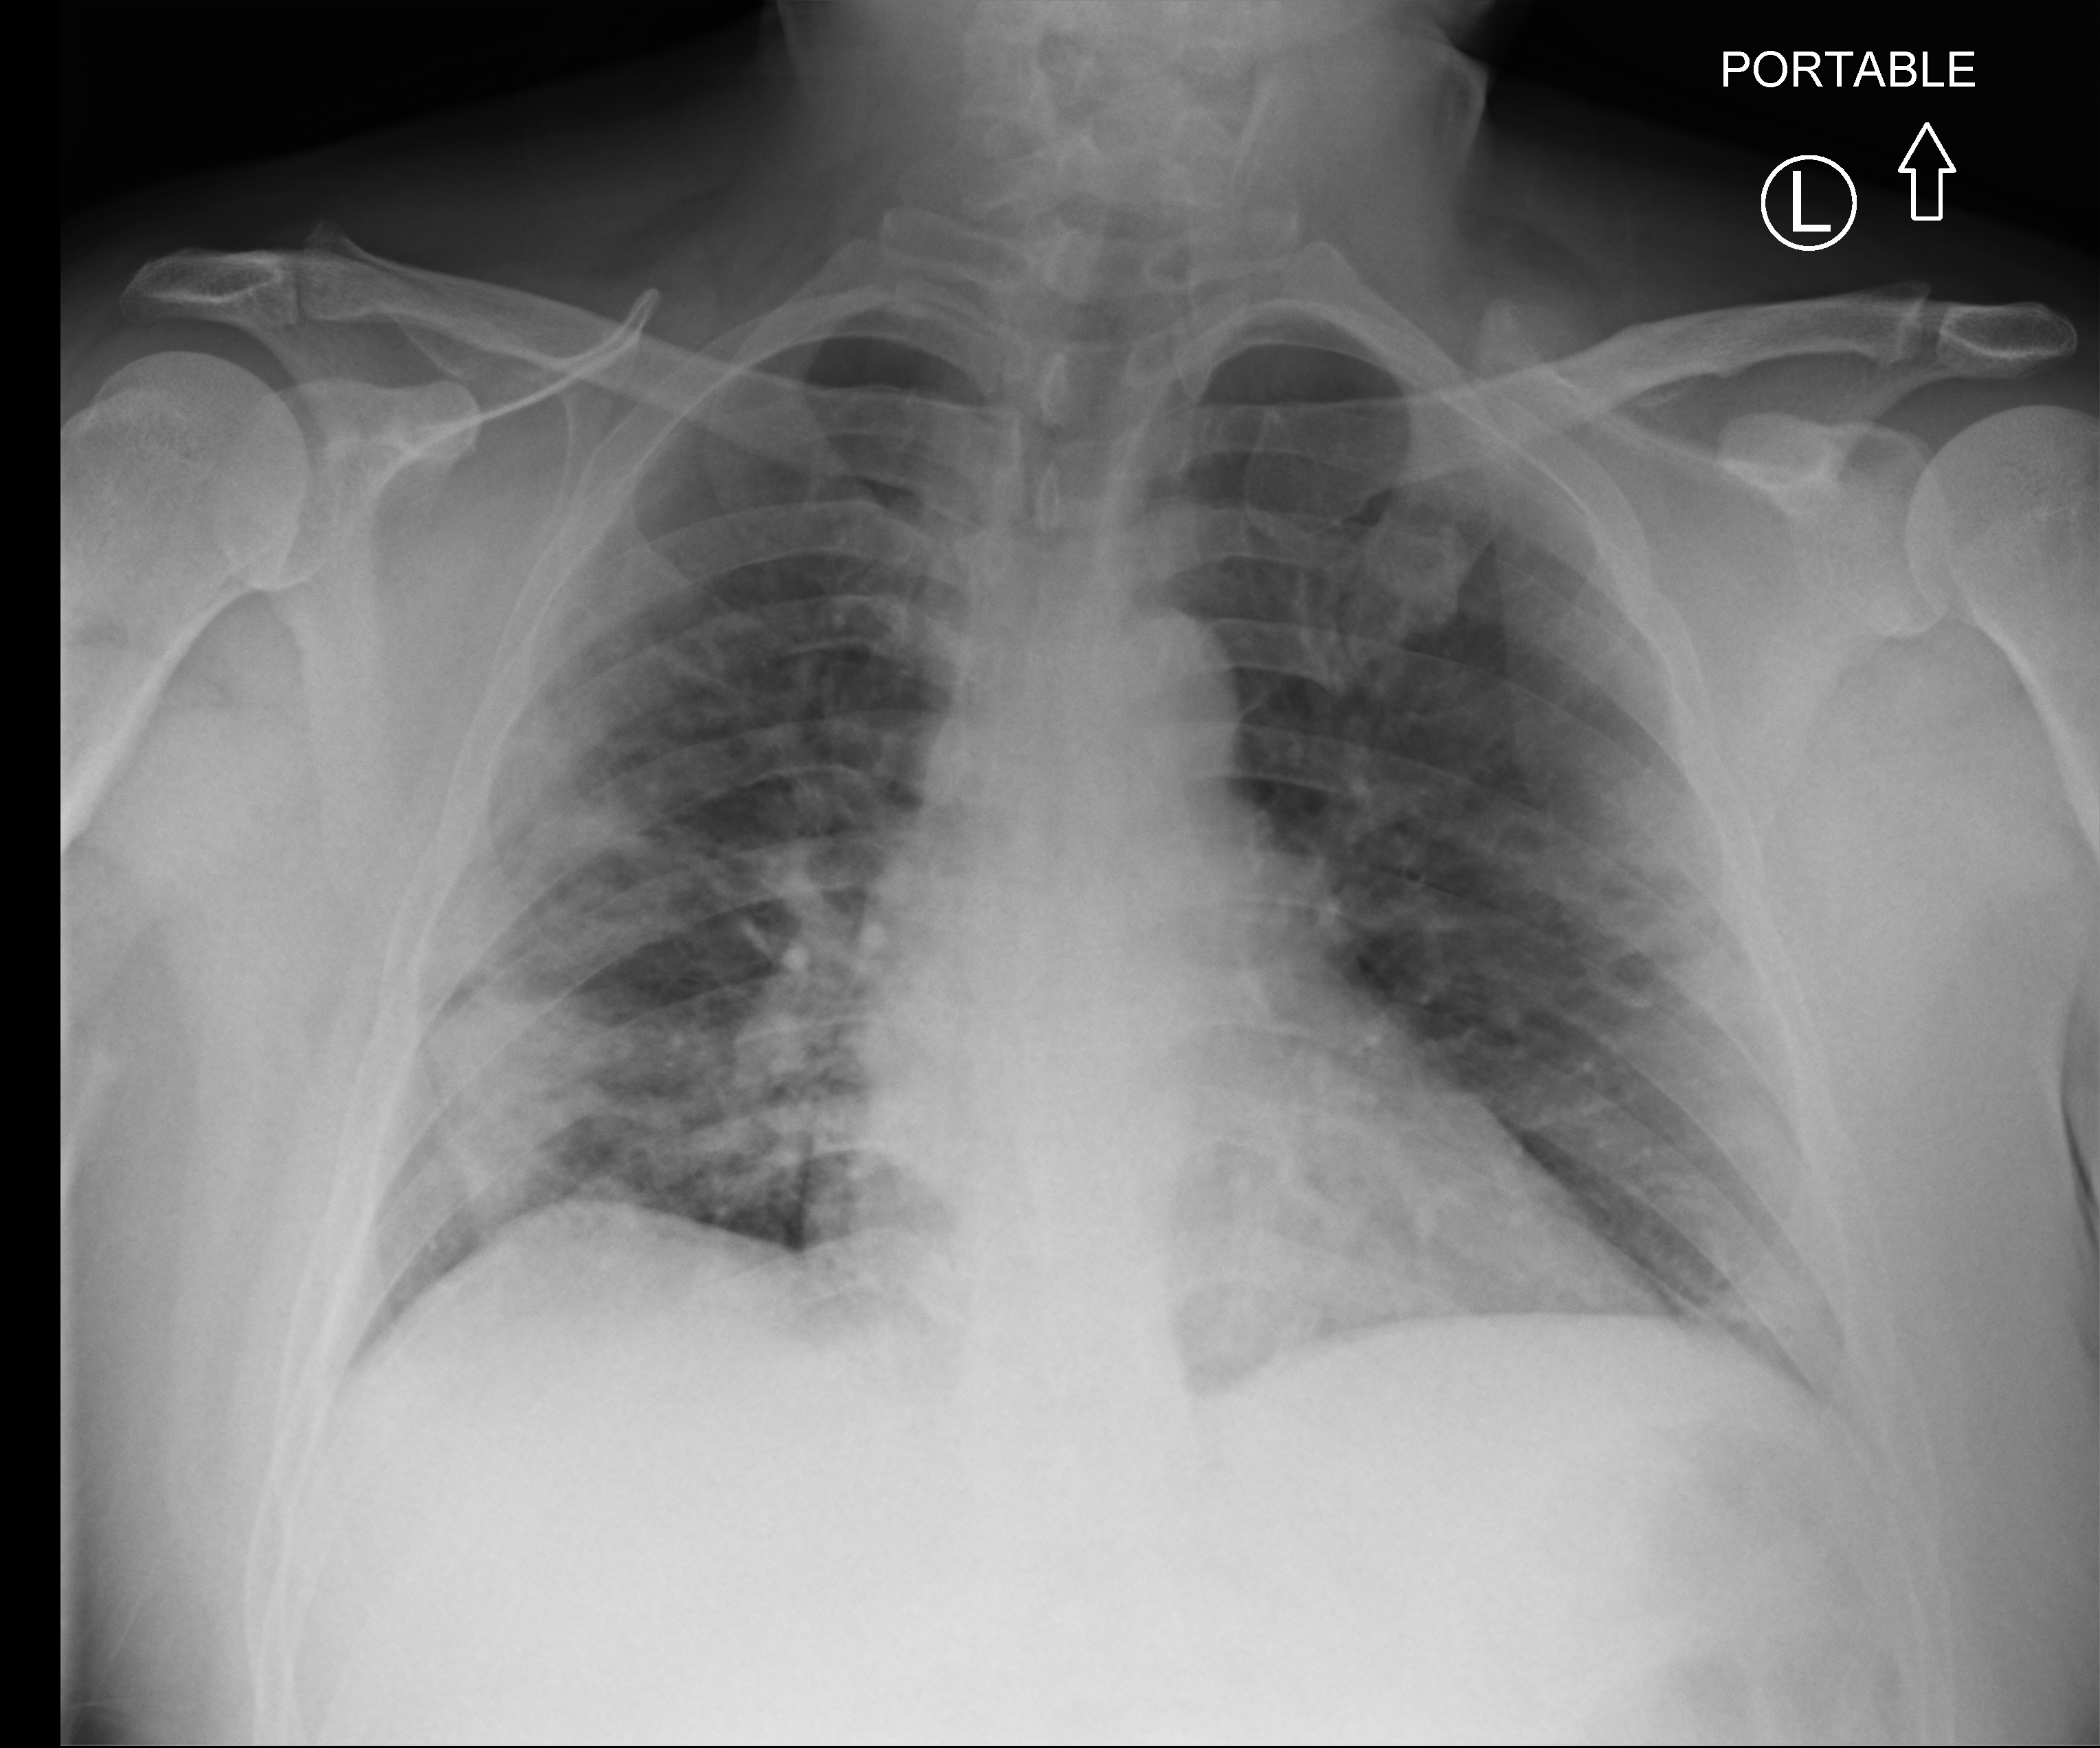
Bedside chest radiograph (computed radiography); anteroposterior (AP) projection. Patient hospitalised with COVID-19; male, aged 18–59 years.
Hospital-stay facts (about this admission, not read from this image; timing relative to this image not recorded): chronic kidney disease (admission record): no; mechanically ventilated during this hospital stay: no.